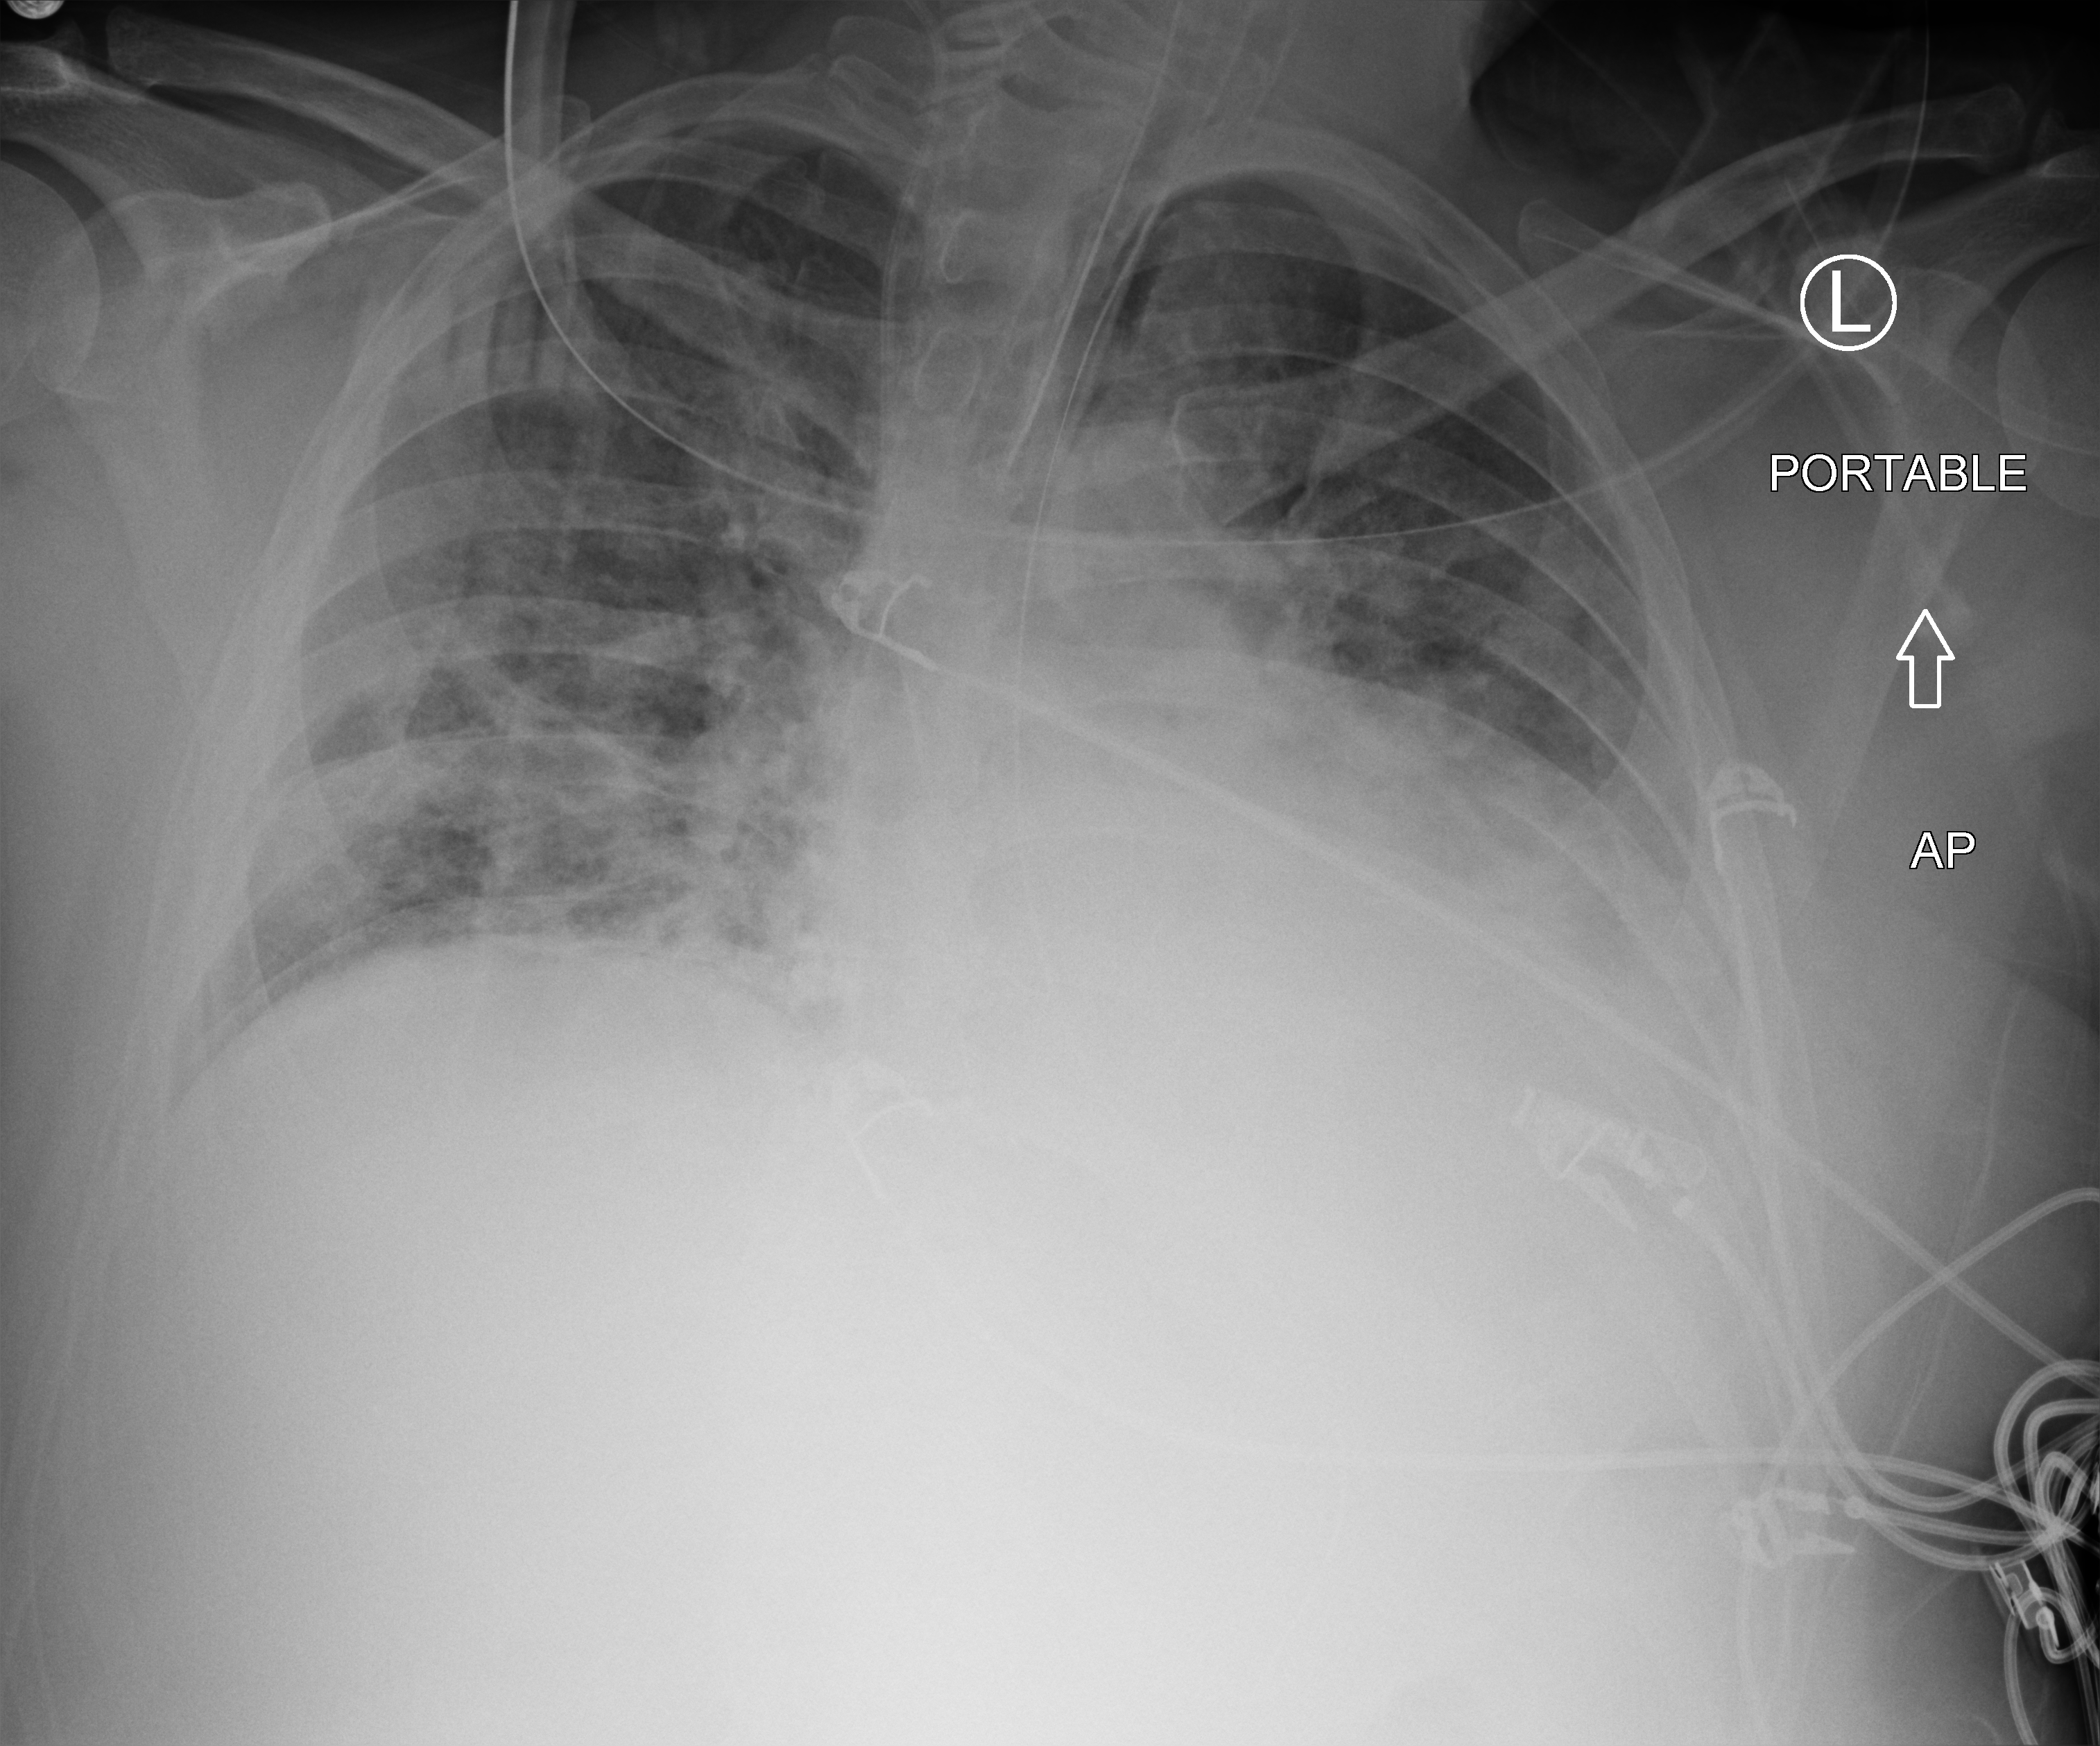
Chest X-ray (portable), anteroposterior (AP) projection. Male patient hospitalised with COVID-19, age 18–59 years.
Admission-level facts for this patient (not findings on this image; timing relative to this image not recorded): length of hospital stay: 39 days.